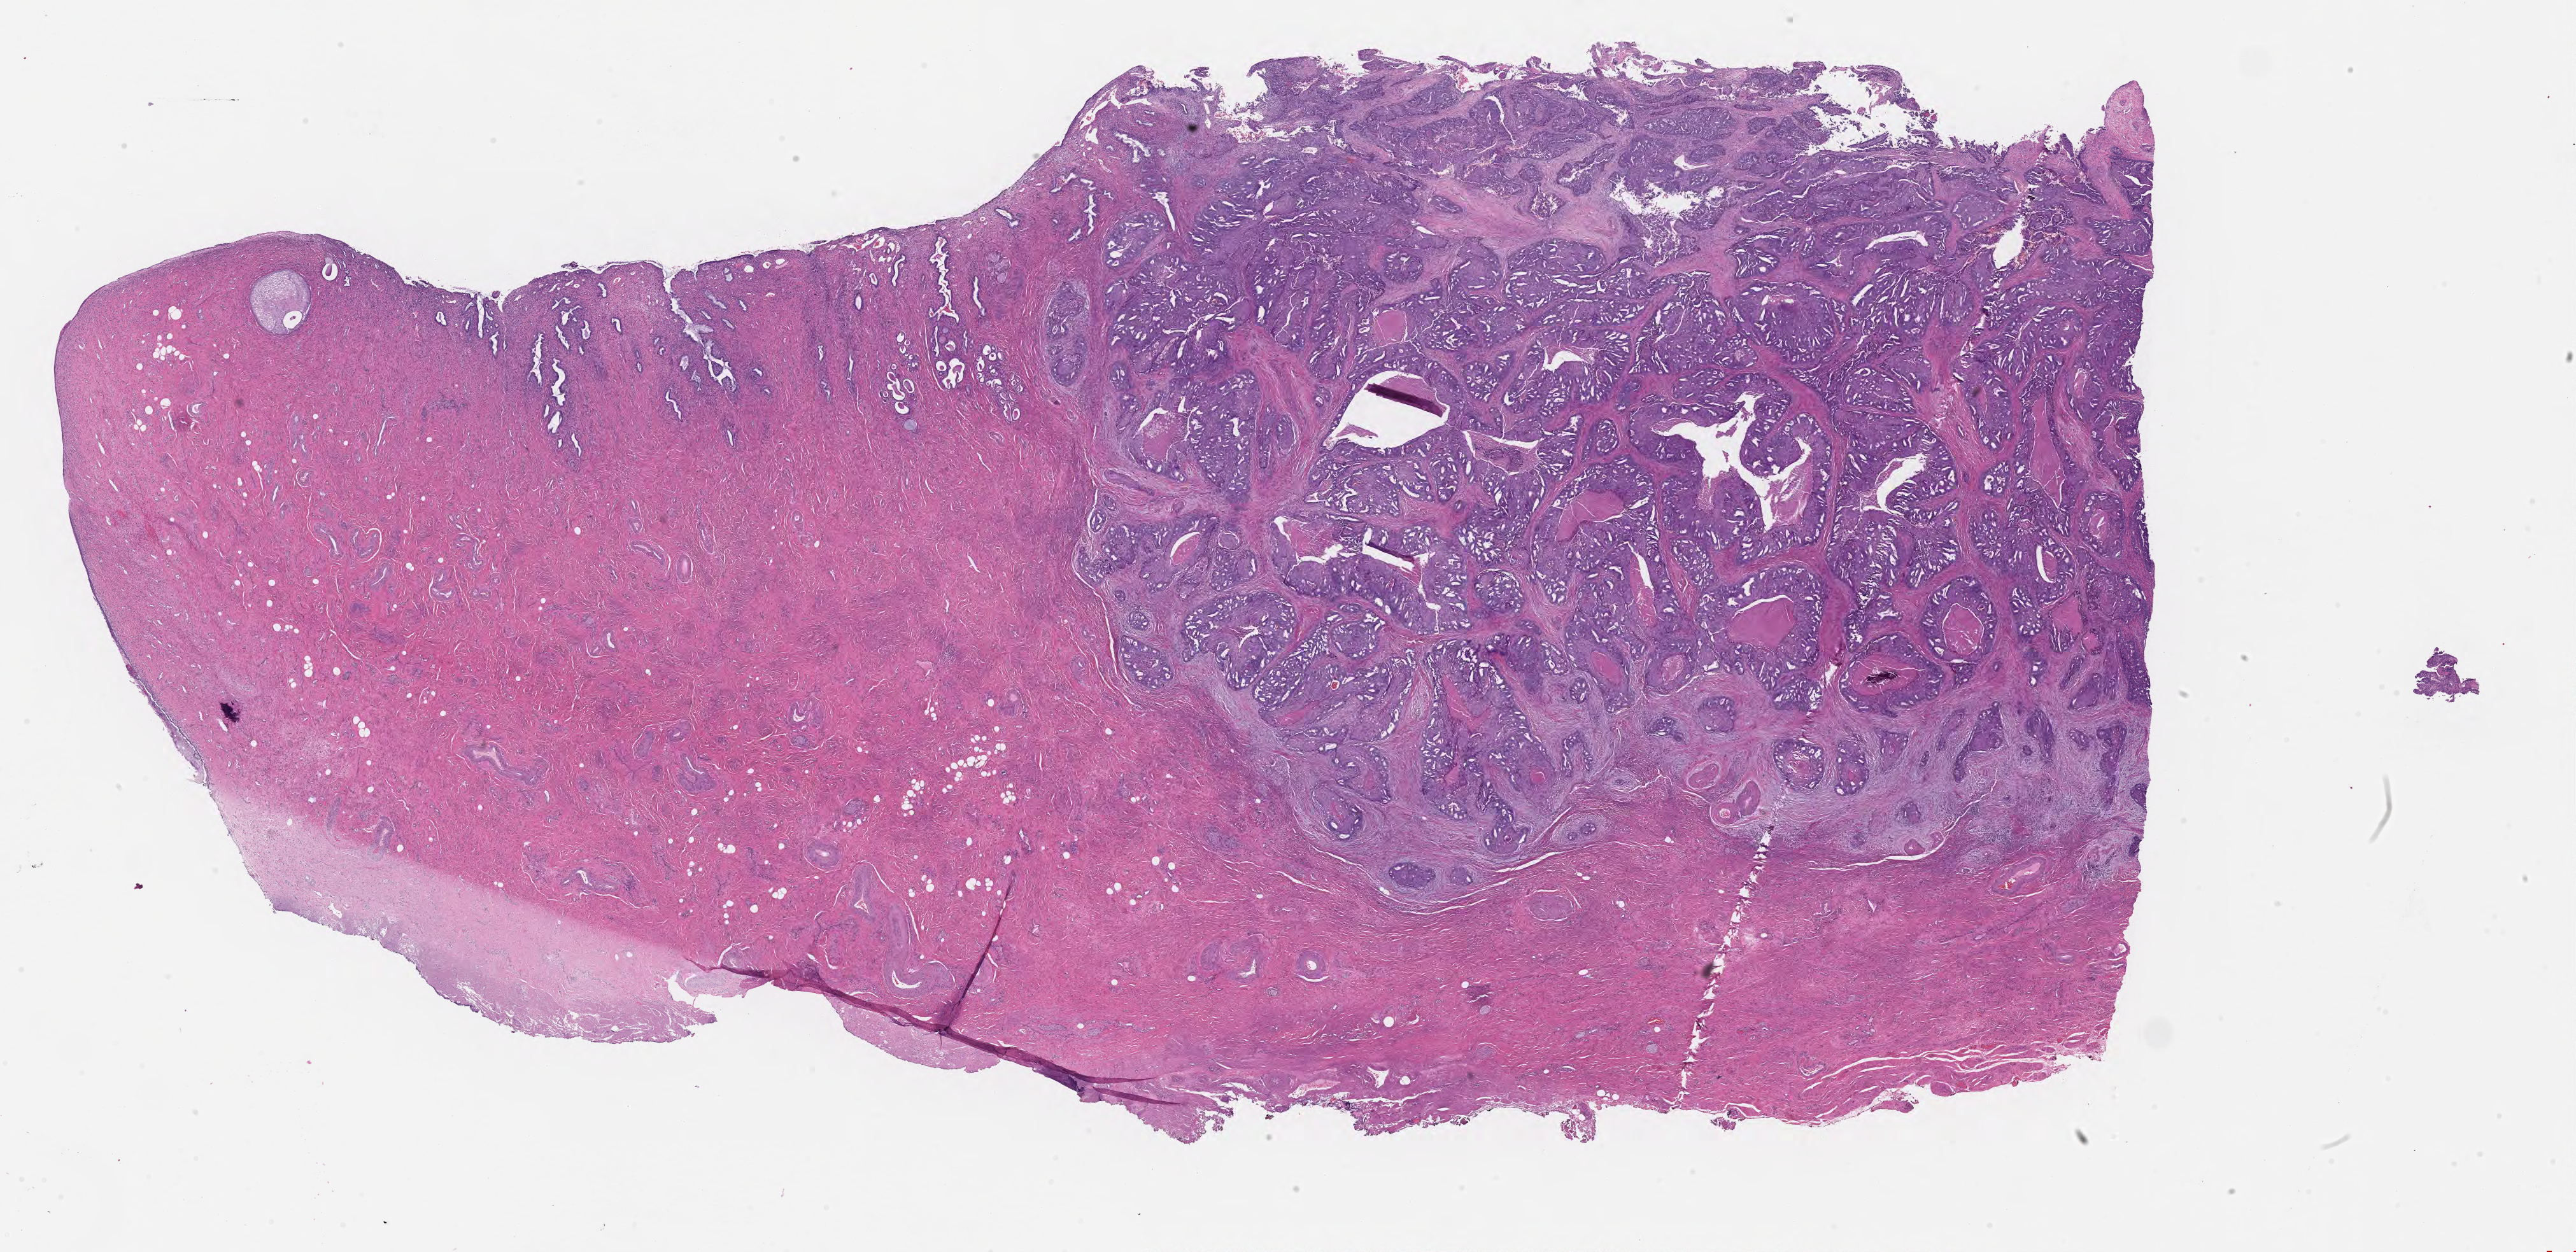
Digitized hematoxylin and eosin (H&E)-stained section — a low-resolution overview of the entire scanned area, about 32.6 x 15.9 mm. FFPE section. Specimen: primary tumor. Site: endometrium. Female patient; age at initial diagnosis 53 years. Tumor grade: G2 (moderately differentiated). Composition of this section per pathologist review: tumor cells 80%, tumor nuclei 80%, stromal cells 13%, necrosis 6%, normal cells 1%. Inflammatory infiltration, as recorded: lymphocyte infiltration 4%, monocyte infiltration 1%, neutrophil infiltration 3%.
AJCC pathologic stage: Stage II. Section: top of the tissue portion. Histologic diagnosis: Endometrioid adenocarcinoma, NOS.